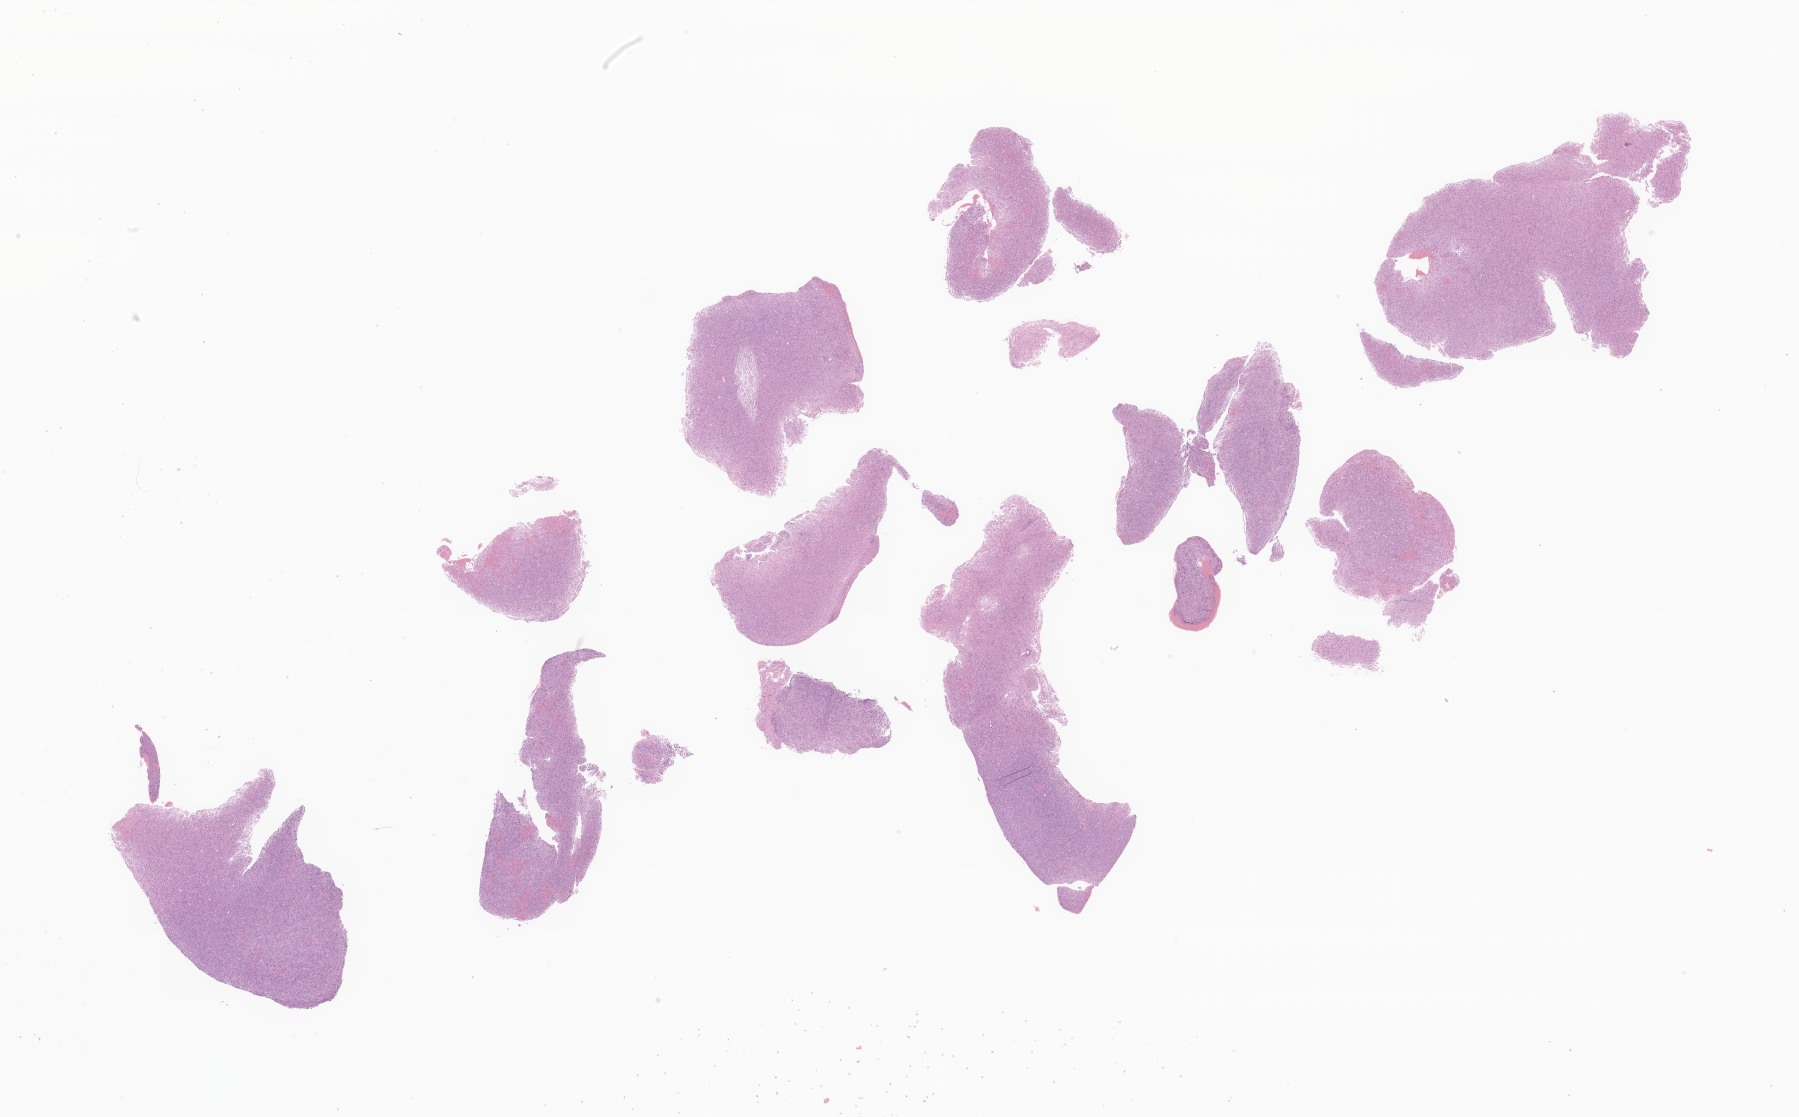
Haematoxylin and eosin whole-slide image of tumor tissue from the parietal lobe — a low-resolution overview of the entire scanned area, about 30.3 x 18.8 mm. FFPE section. Patient male; age 72 months (6 years).
Diagnosis: Glioma, malignant.